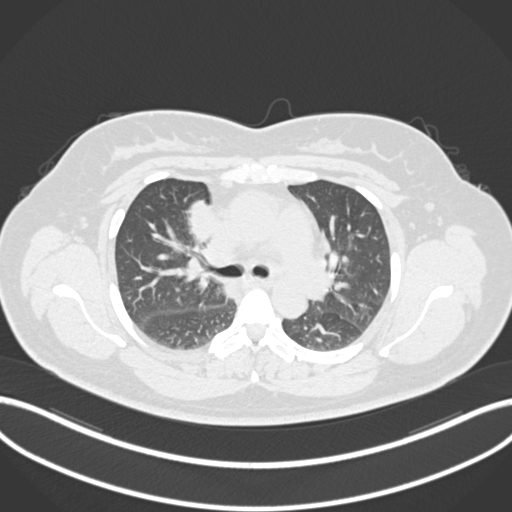
Chest CT, one axial slice. Slice 115 of 183 in the series (ordered by position). Reconstruction kernel B30f. 120 kVp. Lung window (W 1500 / L -600 HU). 1 mm slice thickness. 512 × 512 image matrix. Female patient, age 46 years. From the clinical record (not read from this slice): clinical TNM (as recorded): T2a N1 M0.
Outlined on this slice (rectangle marked by the reading radiologist):
- lung tumour (recorded histology: adenocarcinoma): bounding box (x1, y1, x2, y2) in pixels: (183, 197, 213, 246)